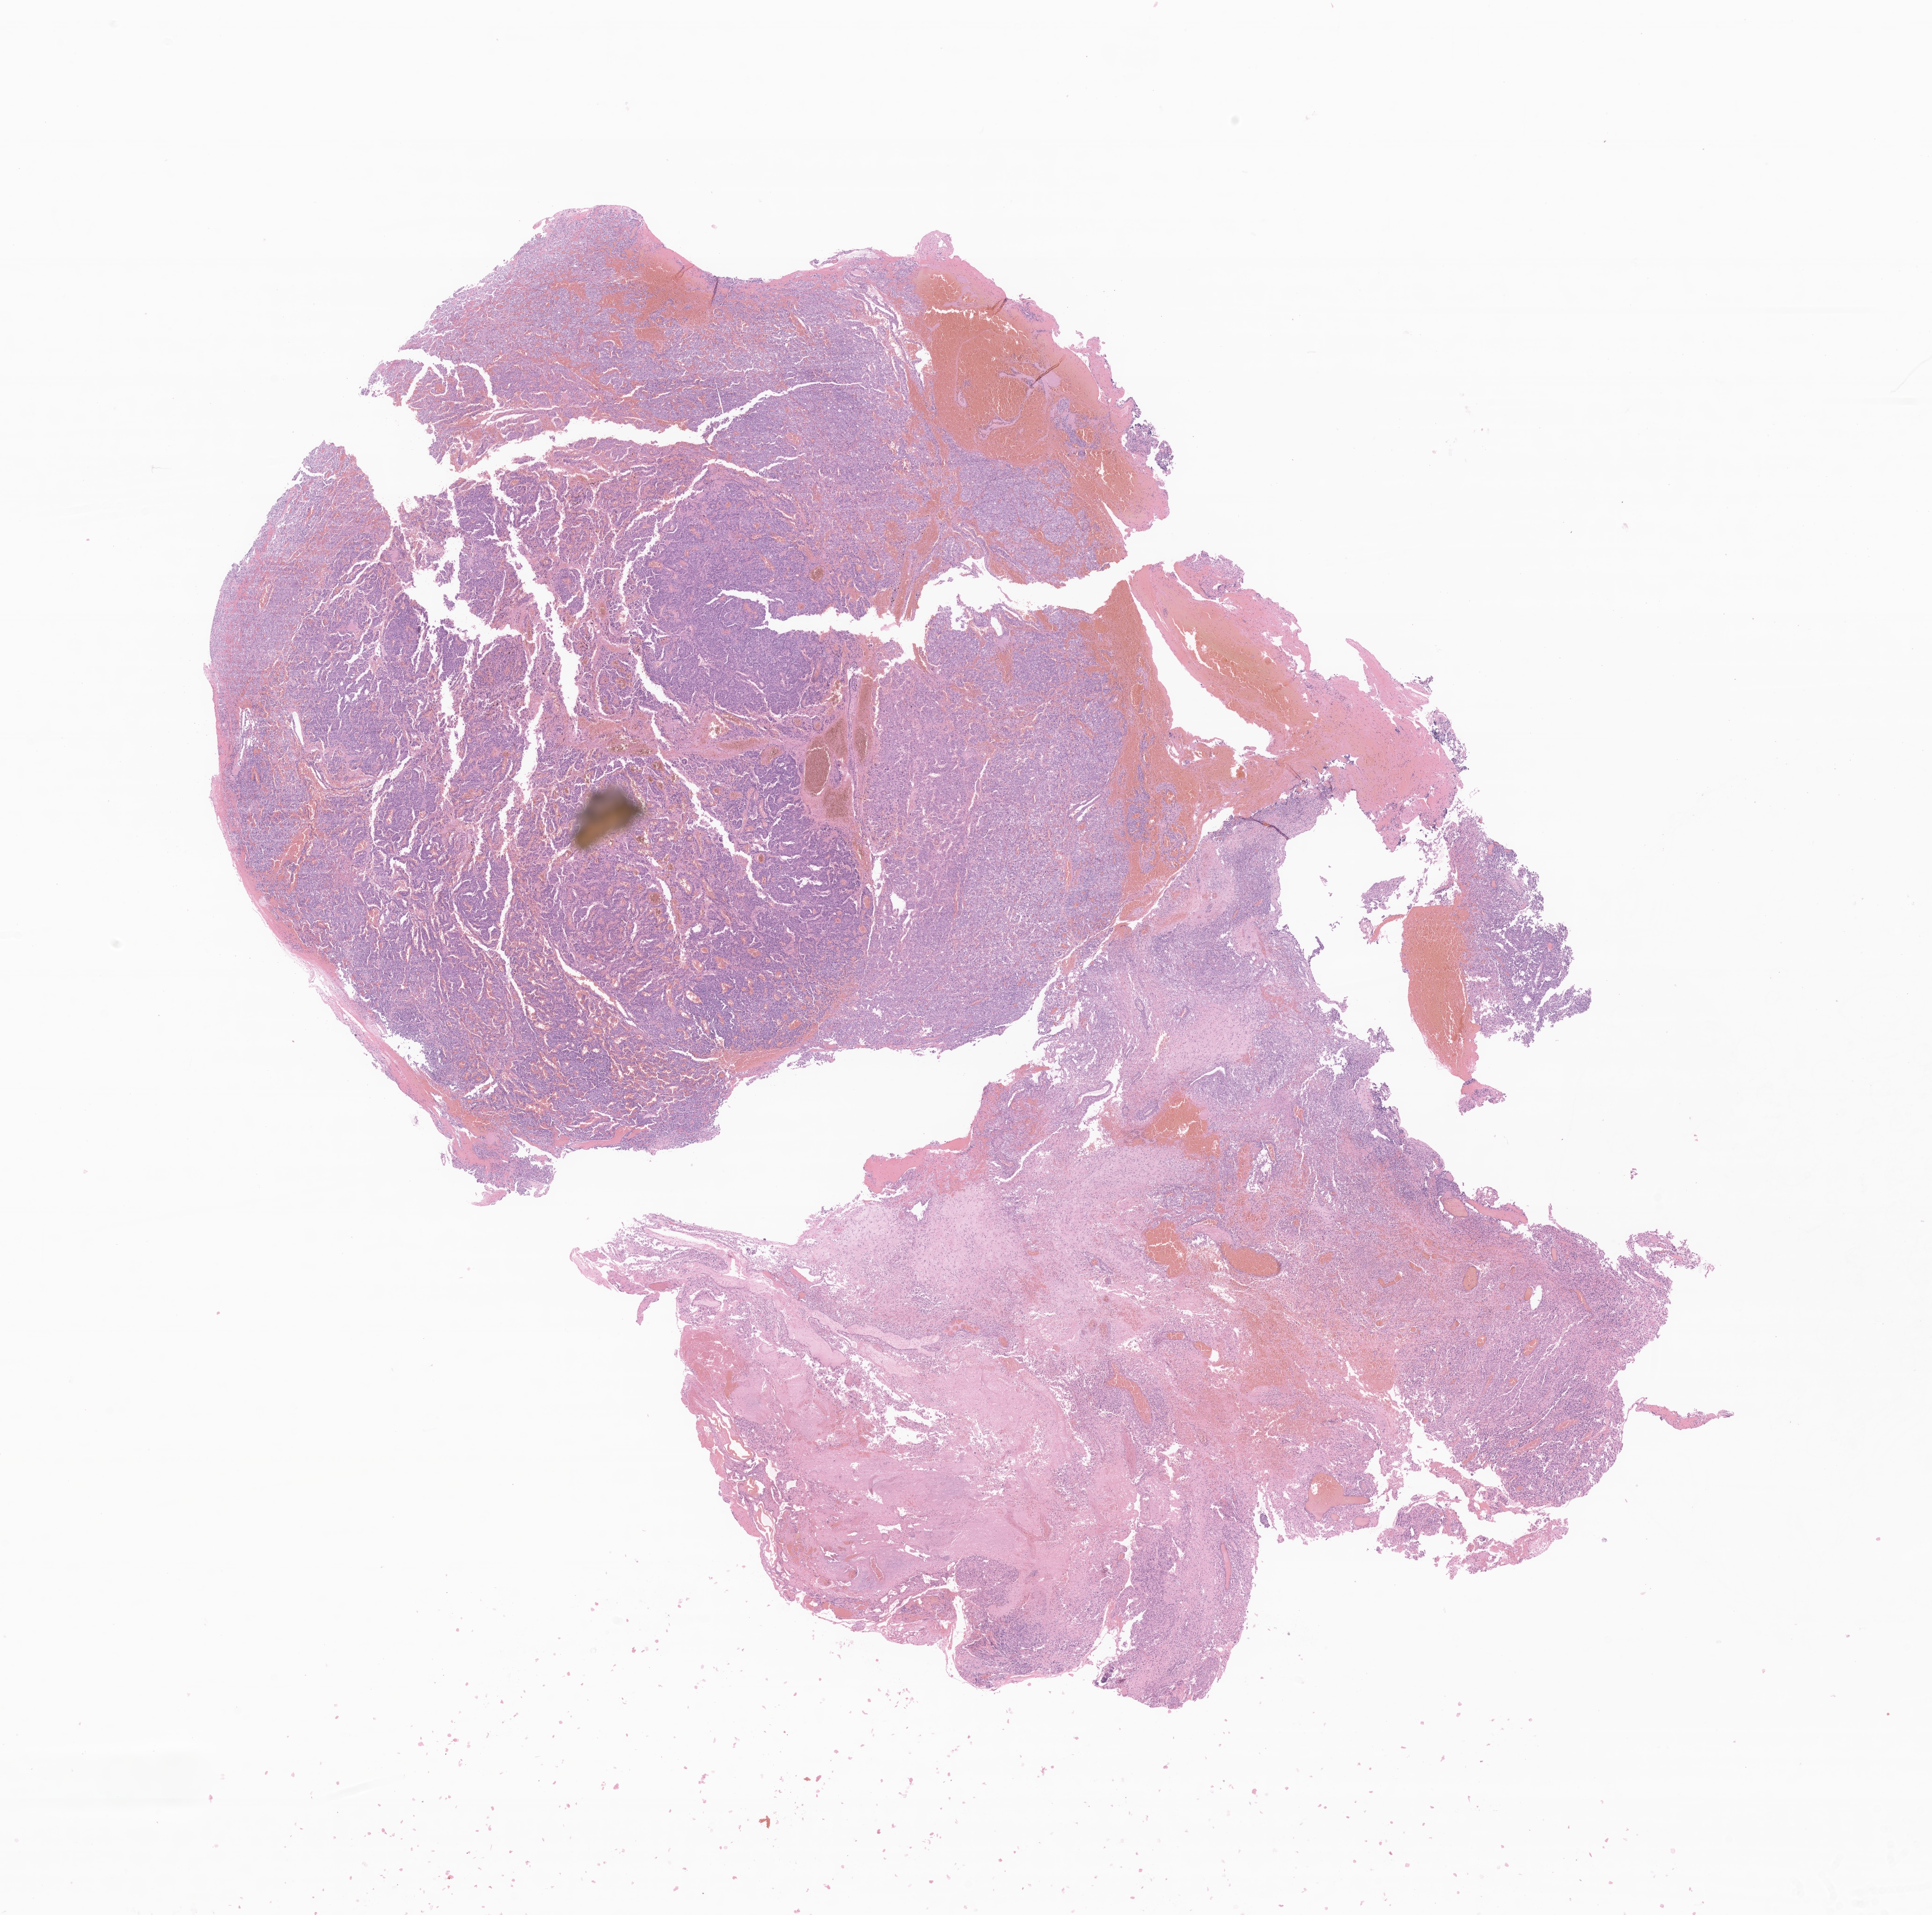
Digitized haematoxylin and eosin-stained section of tumor tissue from the temporal lobe, a low-resolution overview of the entire scanned area, about 17.4 x 17.3 mm; formalin-fixed, paraffin-embedded (FFPE) tissue. Male patient, age 41 months (3 years 5 months).
Diagnosis (ICD-O-3 morphology term): Choroid plexus carcinoma.